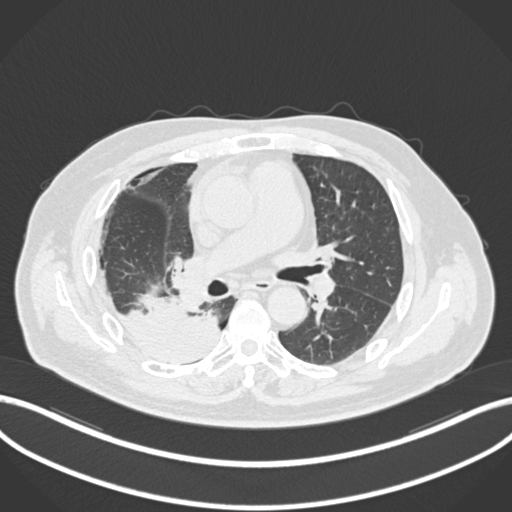
Chest CT, one axial slice; position 105 of 218 along the scan axis; reconstruction kernel B30f; 120 kVp; lung window (W 1500 / L -600 HU); 512 × 512 image matrix. Male patient, age 68 years. From the clinical record (not read from this slice): clinical TNM (as recorded): T2a N0 M0.
Annotated regions visible in this slice (bounding box drawn by a radiologist):
- lung tumour (recorded histology: adenocarcinoma): bounding box <120,292,221,365> (left, top, right, bottom; pixels)